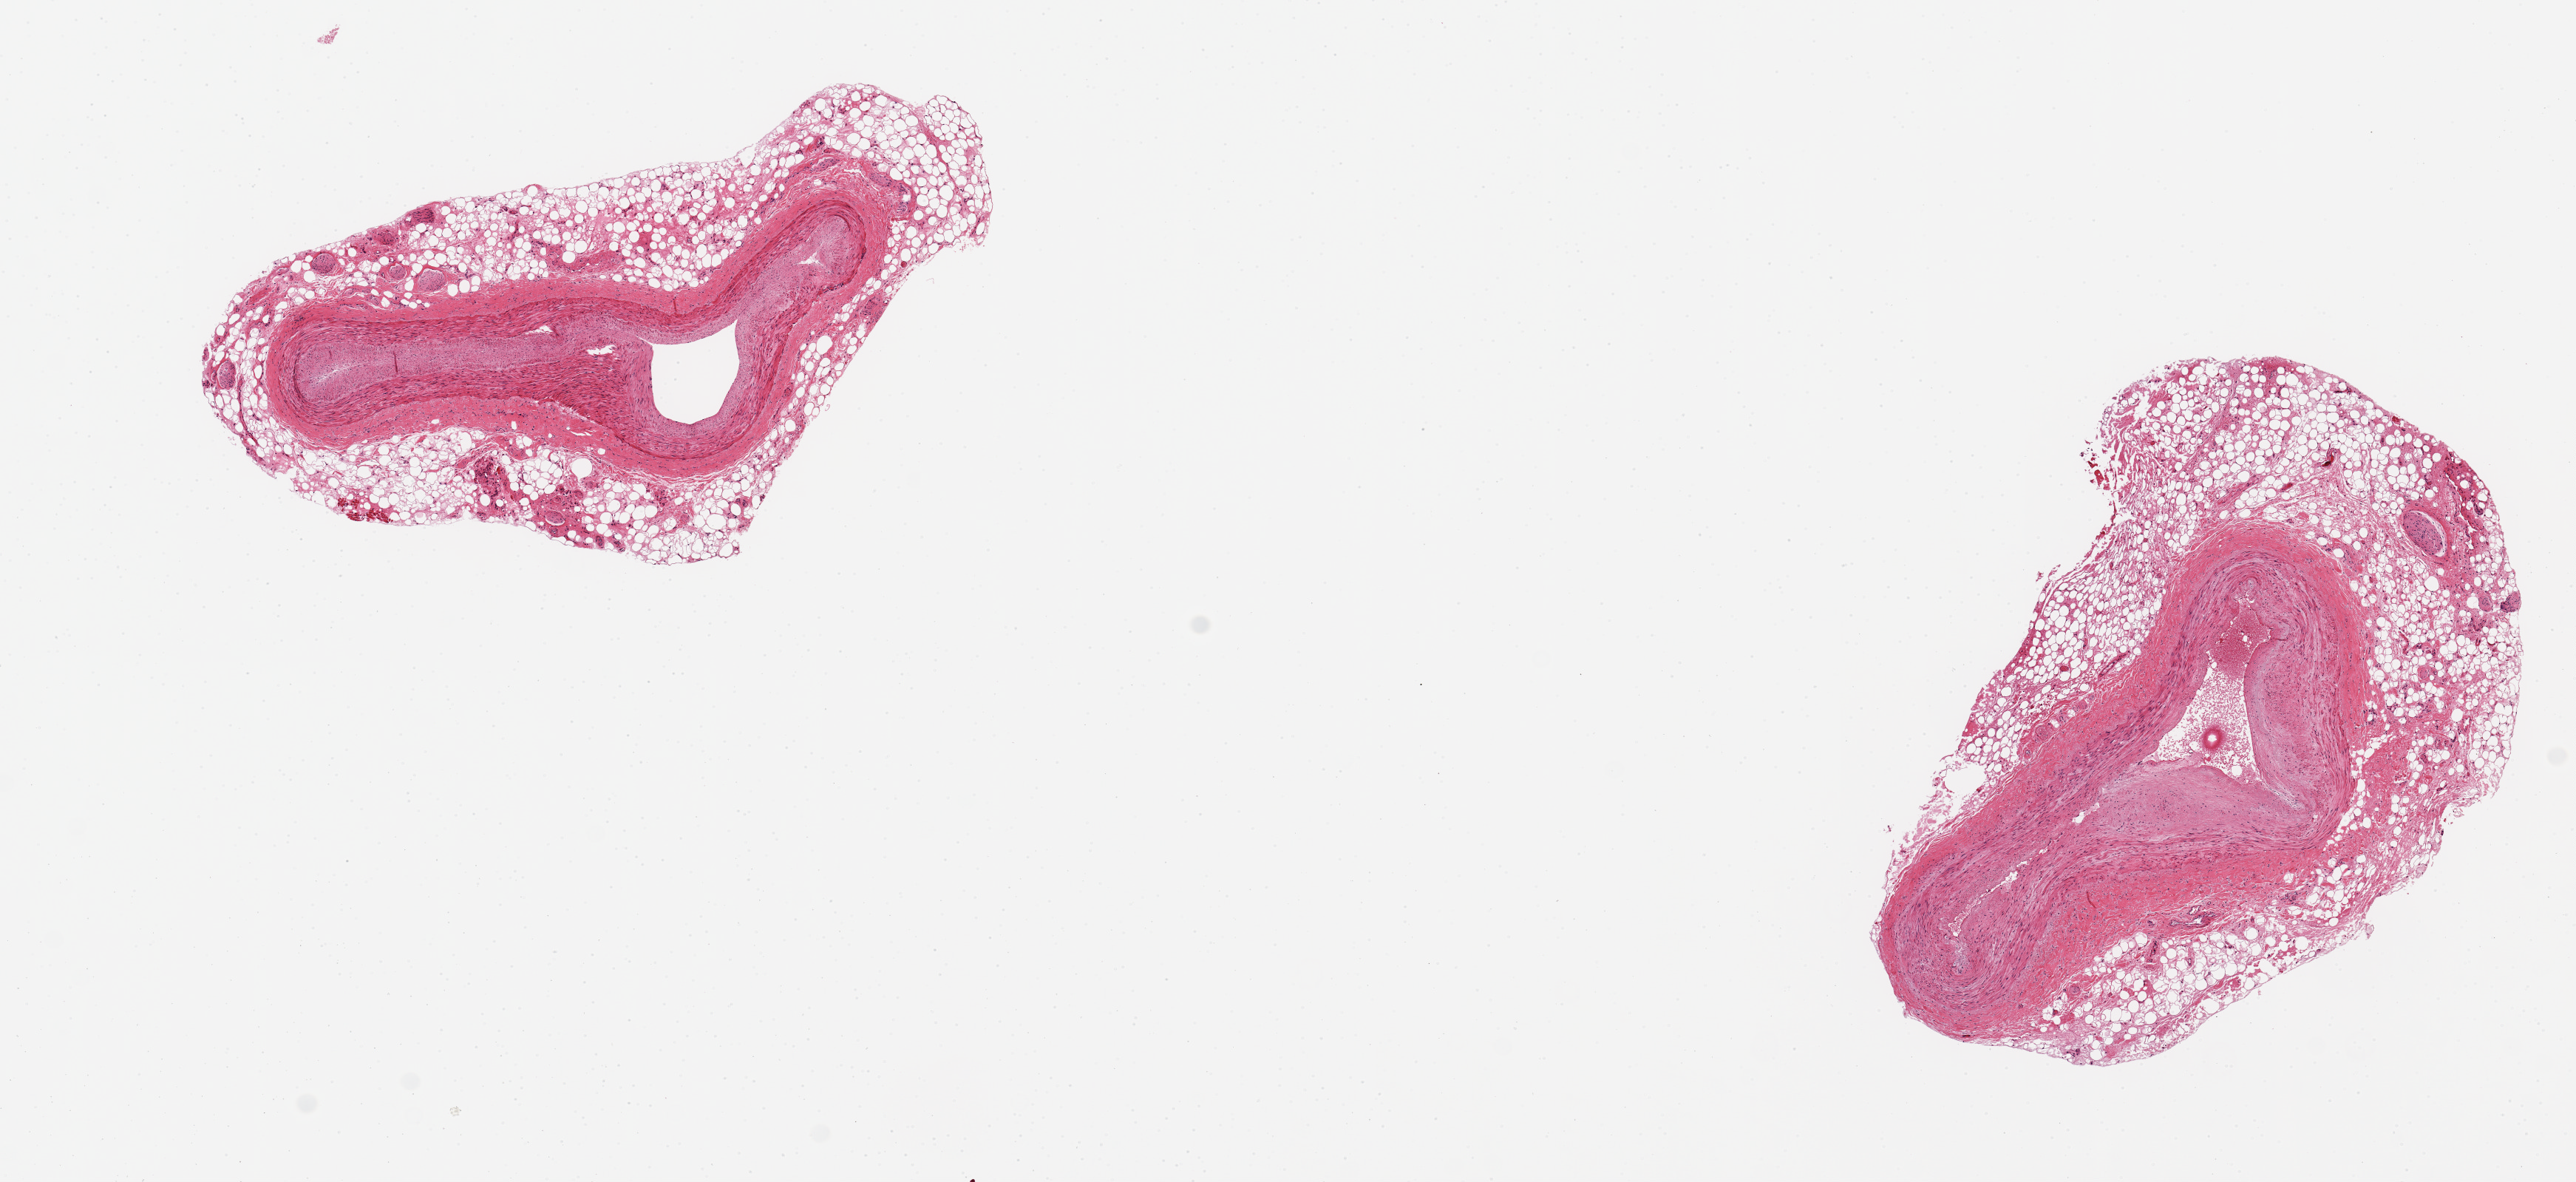
Digitized haematoxylin and eosin-stained section — shown as a low-resolution overview of the whole scanned area (about 13.8 x 6.3 mm, acquisition: 20x scan), PAXgene-fixed paraffin-embedded (PFPE) section, section of coronary artery (target tissue), tissue donor sample. Female donor.
Pathologist's review note for this sample: 2 ~3x0.5mm aliquots, each with 0.5-1mm layer of fat, to much adherent fat.